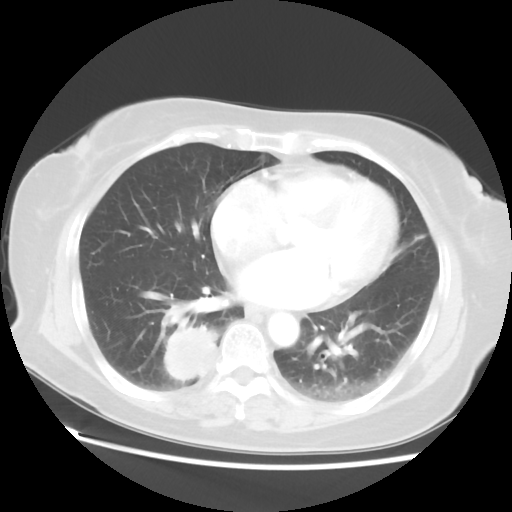
Chest CT, one axial slice; position 22 of 52 along the scan axis; 120 kVp; lung window (W 1500 / L -600 HU); 512 × 512 image matrix. Patient: female, 69 years. Case-level facts recorded for this patient, not image findings: clinical TNM (as recorded): T2 N1 M1a.
Annotated regions visible in this slice (rectangle marked by the reading radiologist):
- lung tumour (recorded histology: adenocarcinoma): box from (x=159, y=319) to (x=222, y=386) px